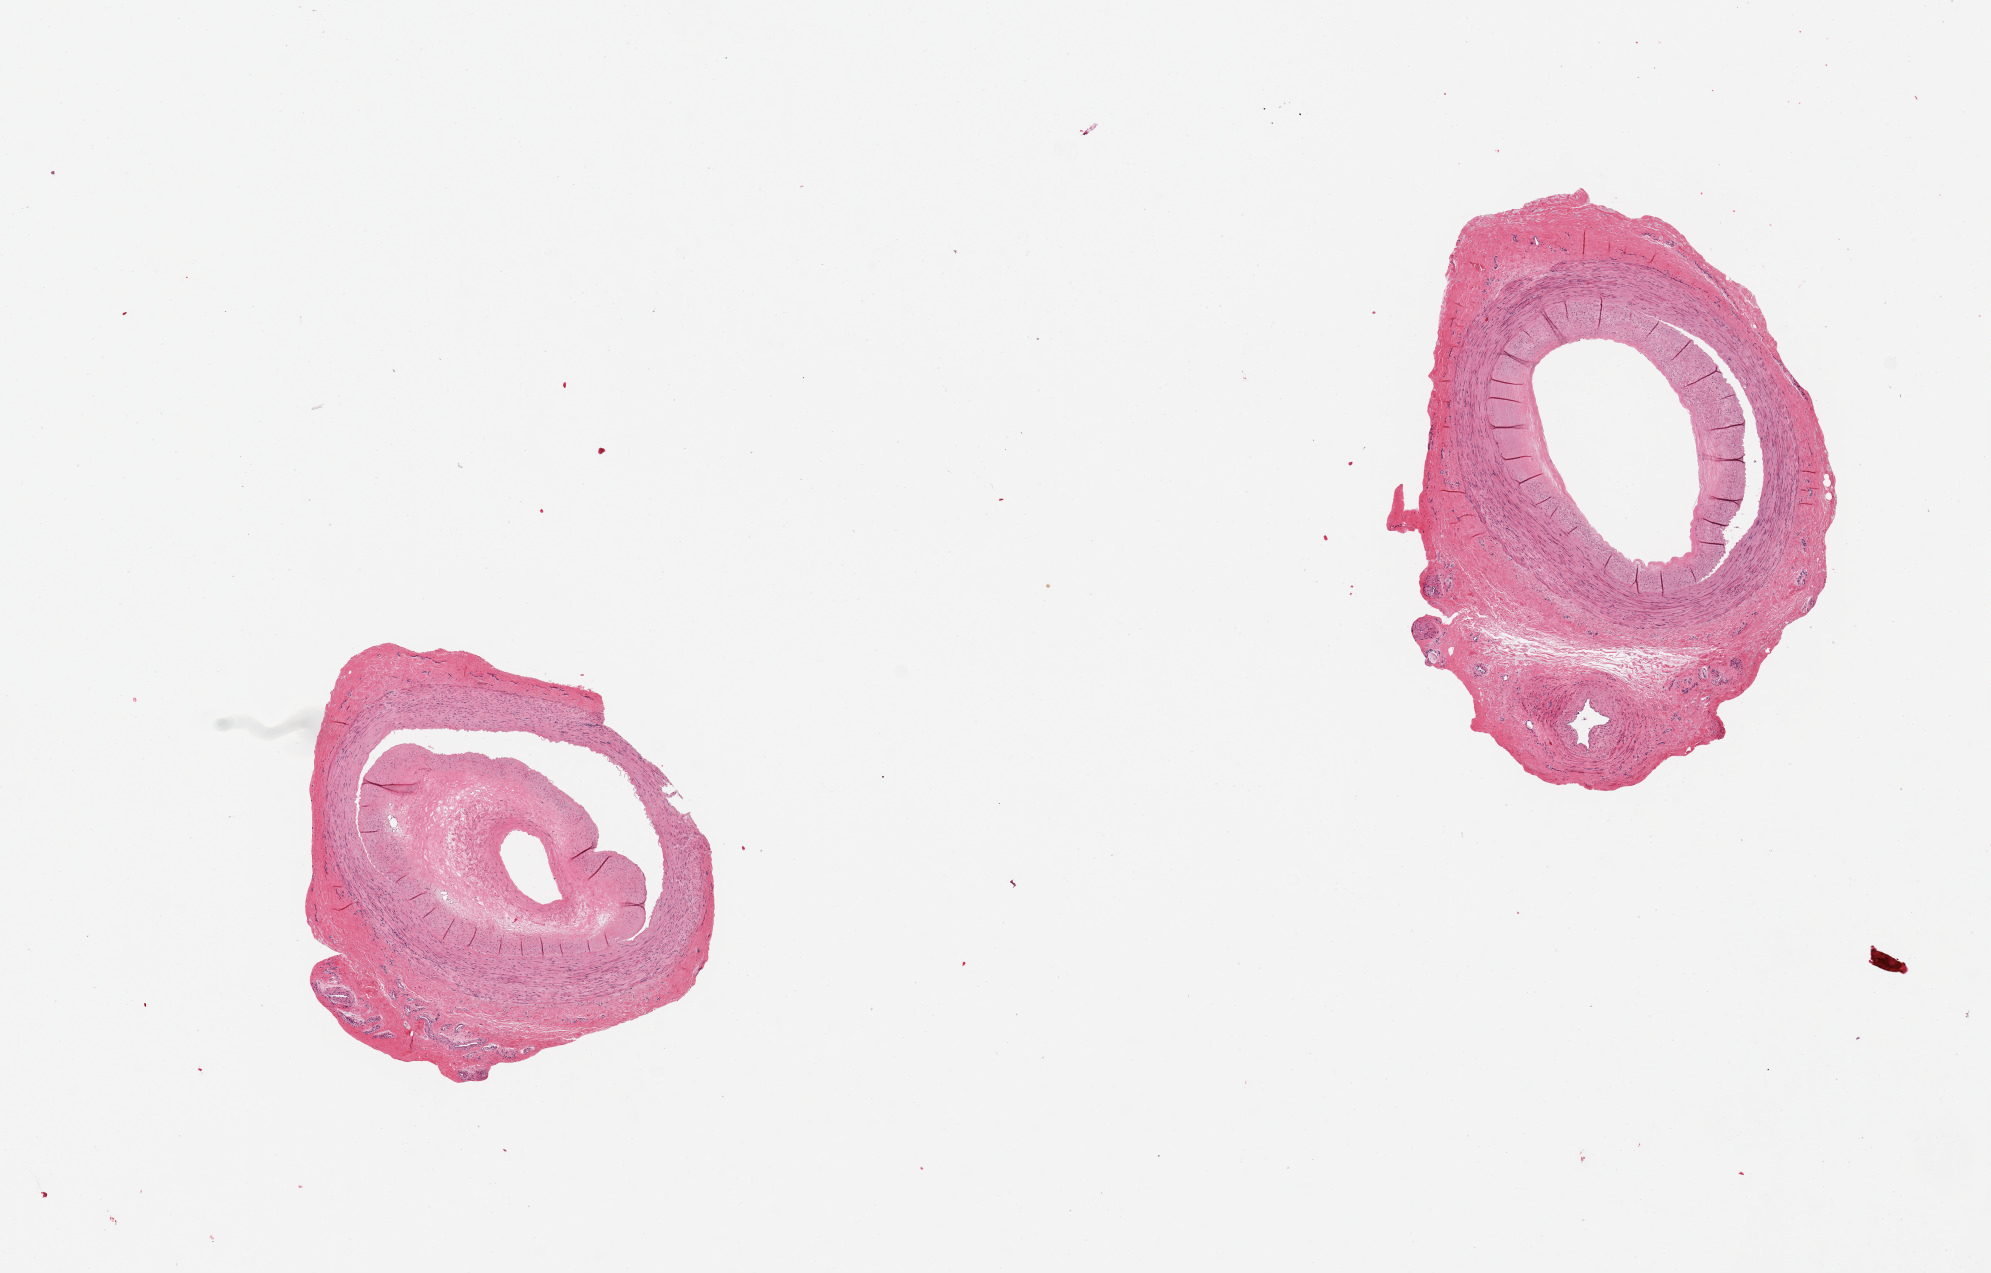
Whole-slide image, haematoxylin and eosin stain — low-resolution overview of the scanned area, about 15.8 x 10.1 mm; PAXgene-fixed paraffin-embedded (PFPE) section; section of tibial artery (target tissue); donor tissue sample. Male donor.
Reviewer comment on this tissue sample: 2 pieces. Moderate to severe atherosclerosis with up to 90% occlusion.